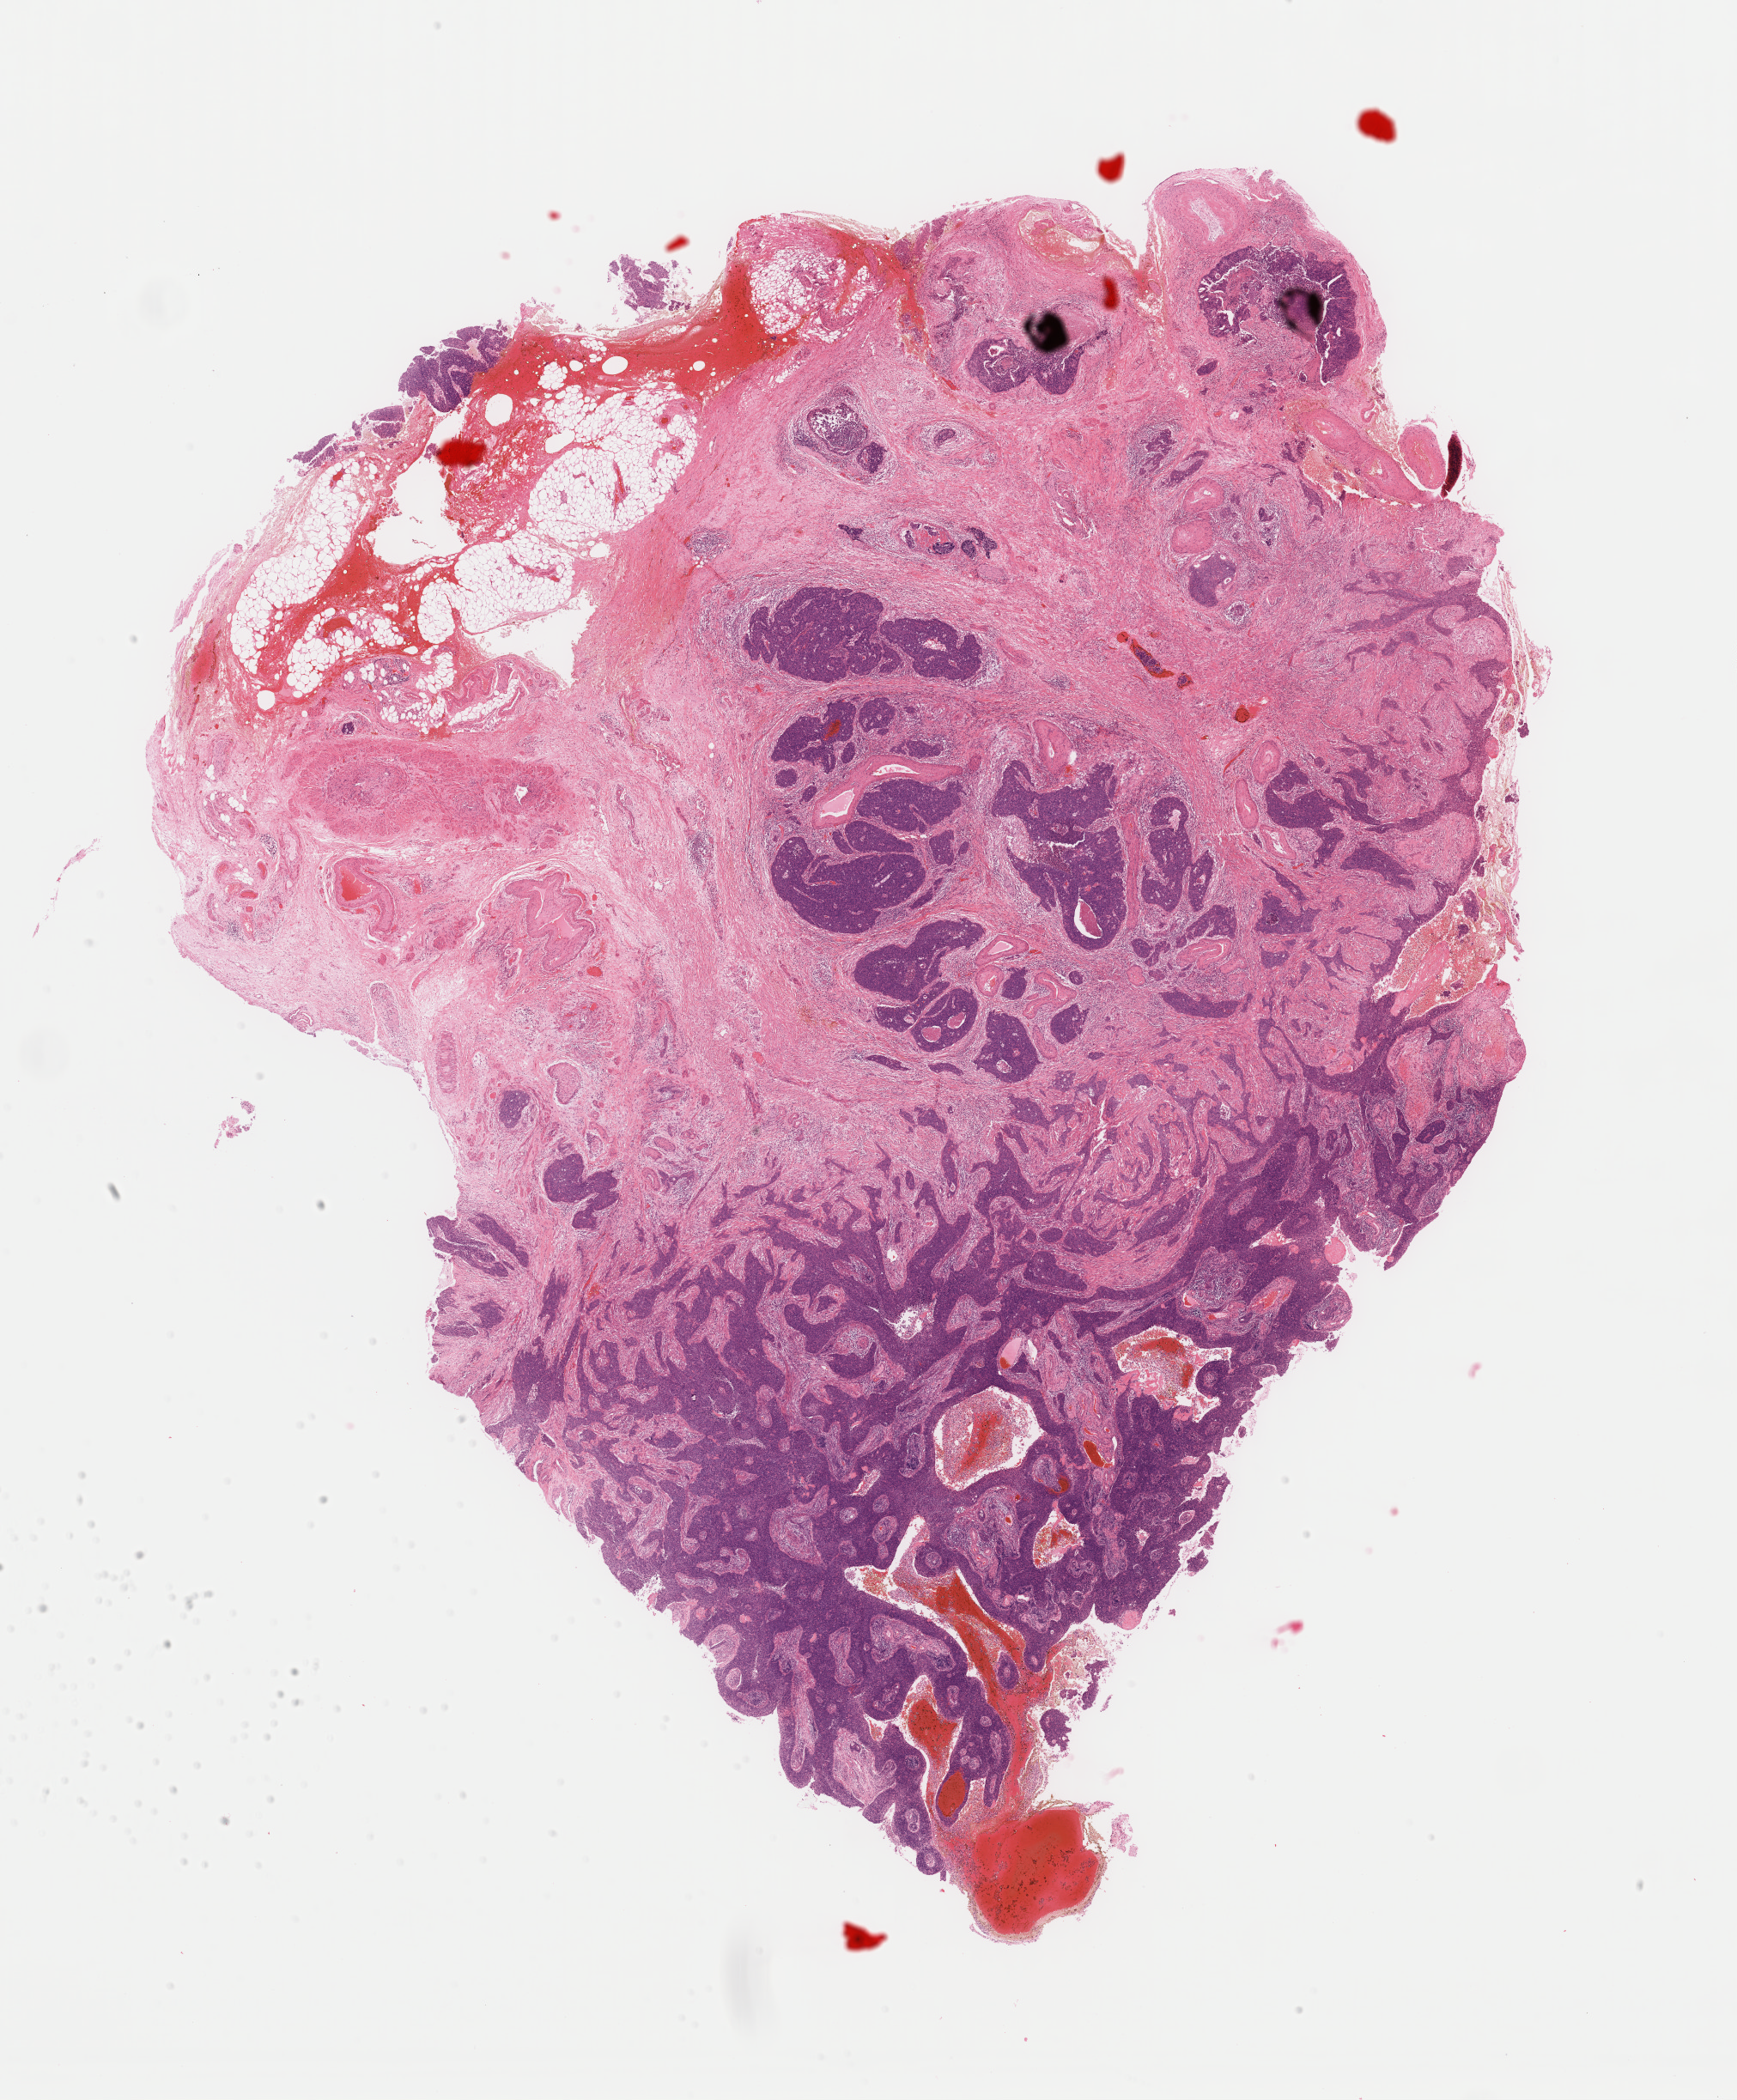
Digitized H&E tissue section (whole slide) — a low-resolution overview of the entire scanned area, about 16.0 x 19.3 mm (acquisition: 40x scan), FFPE section, primary tumour sample from the cervix. Female patient; age at initial diagnosis 50 years. Histologic grade: G3 (poorly differentiated).
FIGO stage: IIA1. Histologic diagnosis: Squamous cell carcinoma, NOS (cervix uteri).